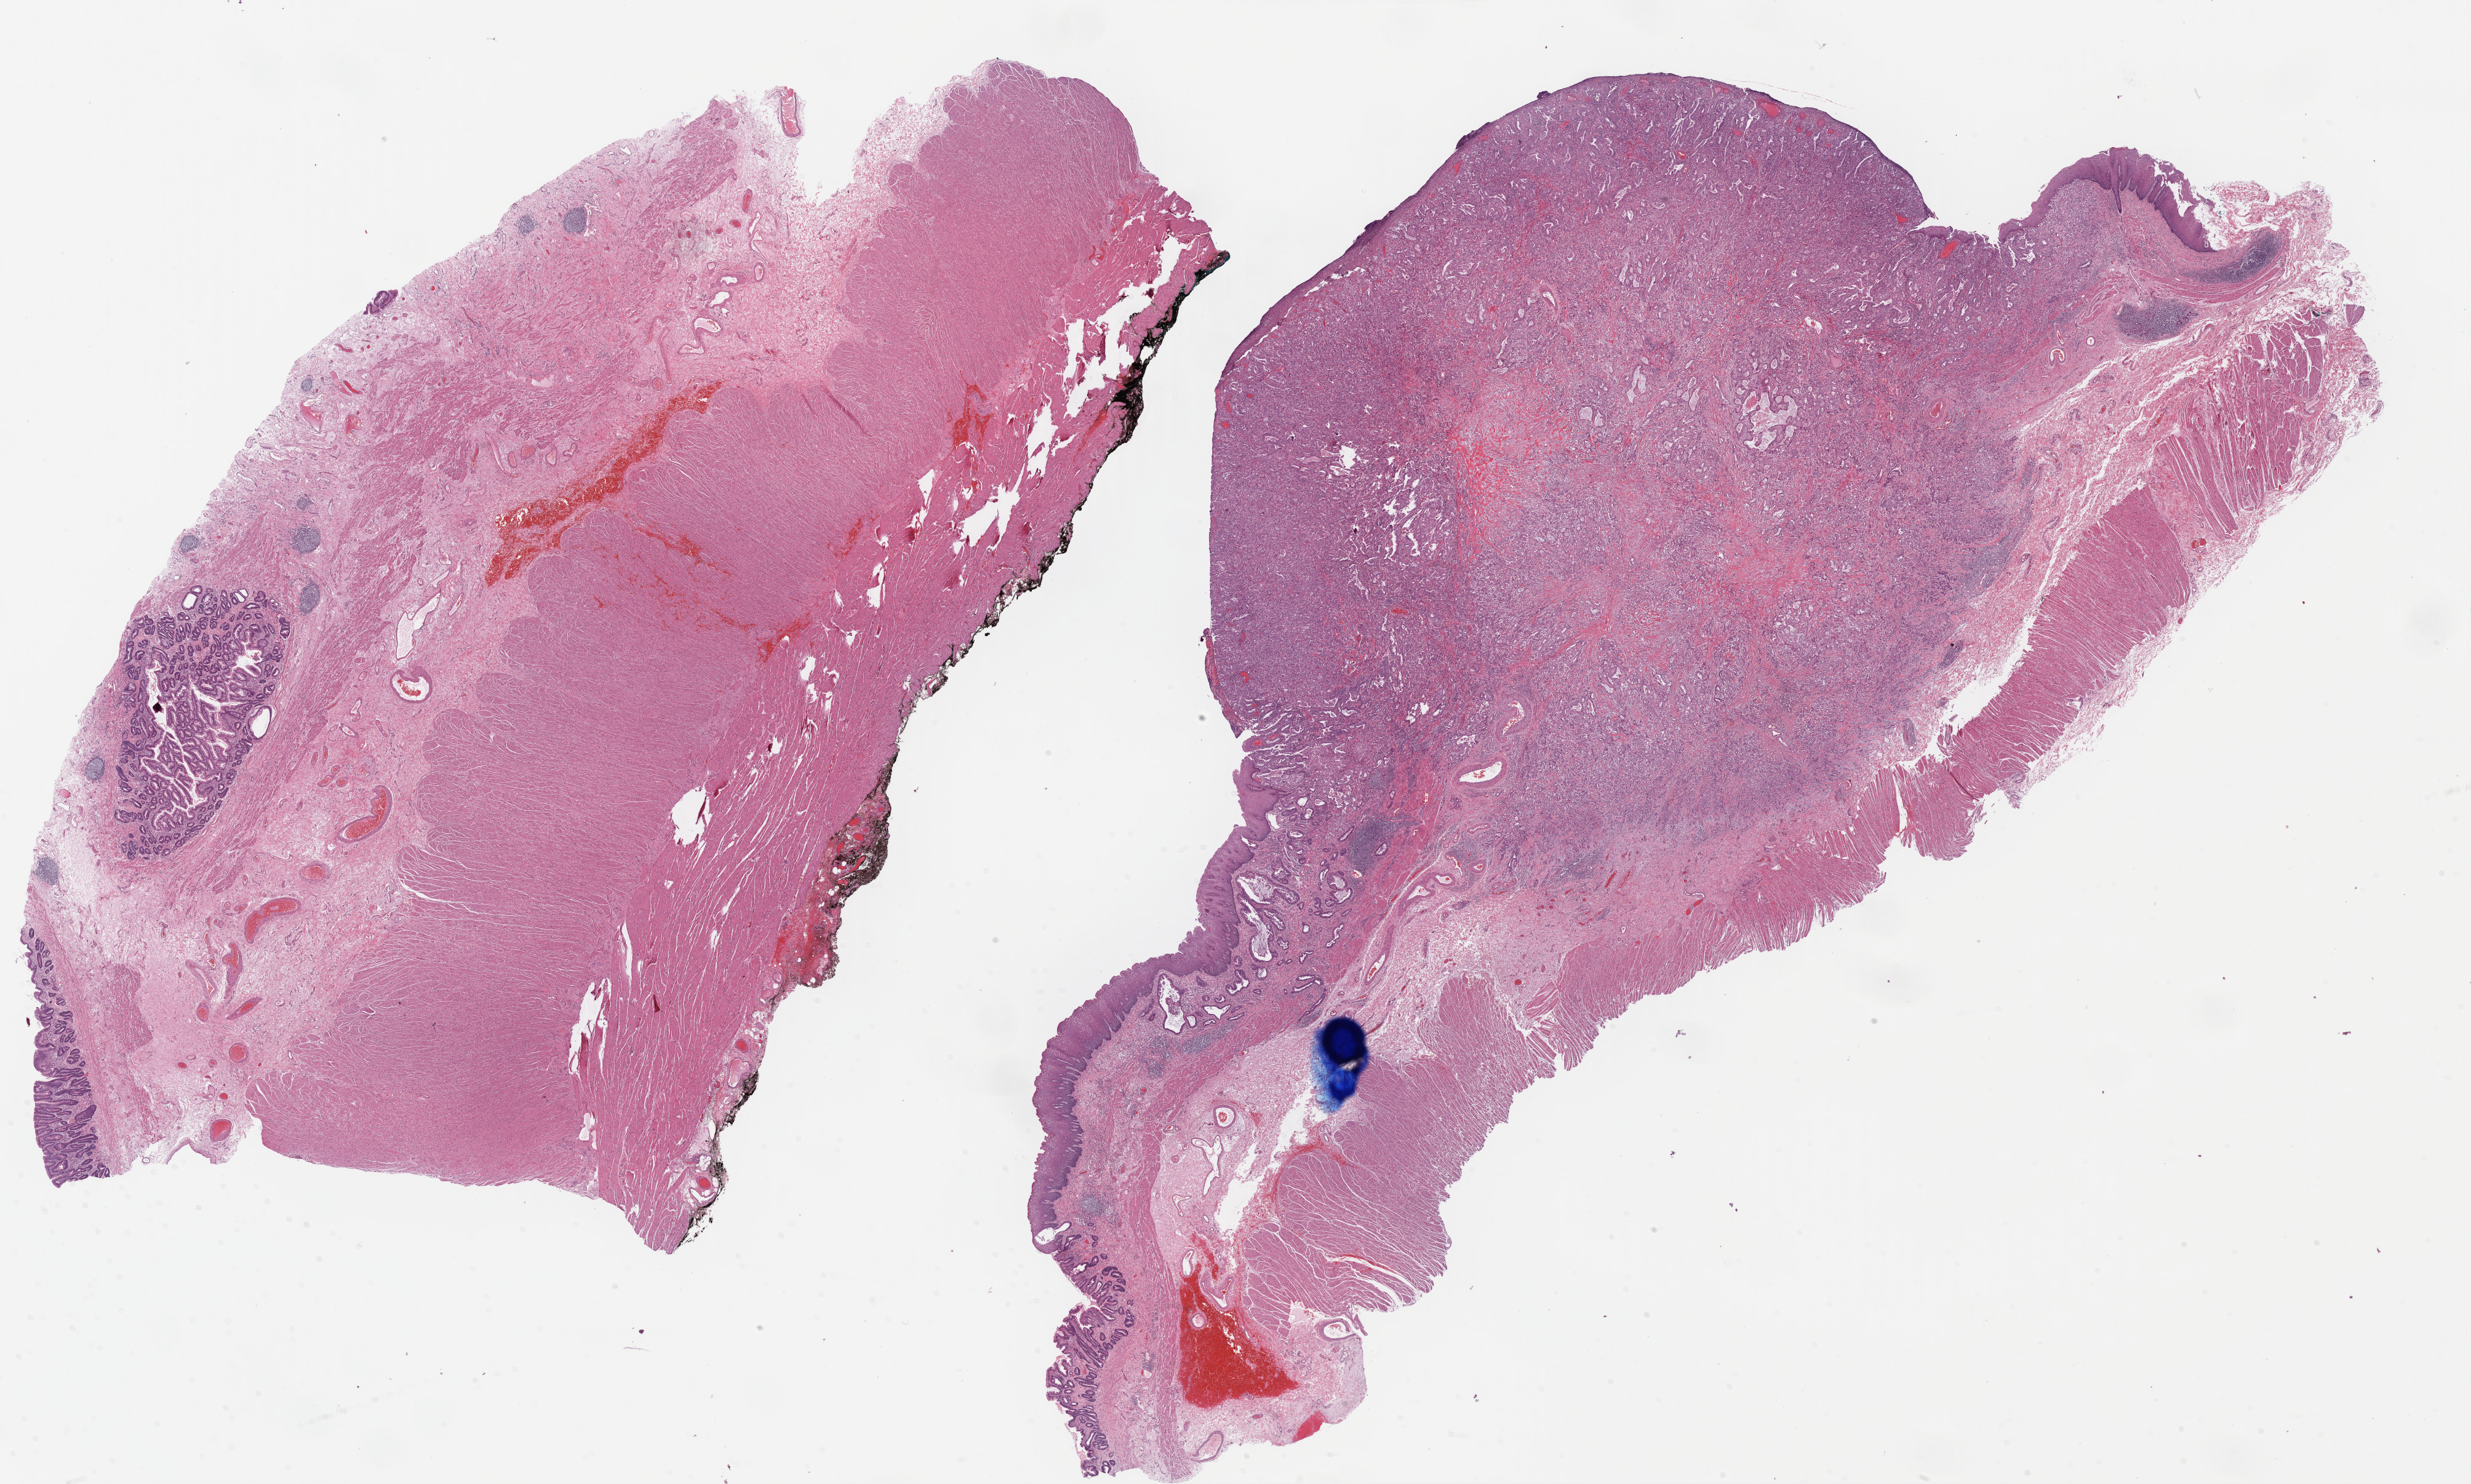
Digitized H&E tissue section (whole slide) — shown as a low-resolution overview of the whole scanned area (about 31.6 x 19.0 mm, slide scanned at 40x), formalin-fixed paraffin-embedded (FFPE) diagnostic section, esophagus, primary tumour sample. Female patient; age at initial diagnosis 70 years. Histologic grade: G3 (poorly differentiated).
Lymph nodes positive (case pathology): 0 of 16 examined. AJCC pathologic stage: I (7th edition). Histologic diagnosis: Adenocarcinoma, NOS (lower third of esophagus). TNM: T1 N0 M0.